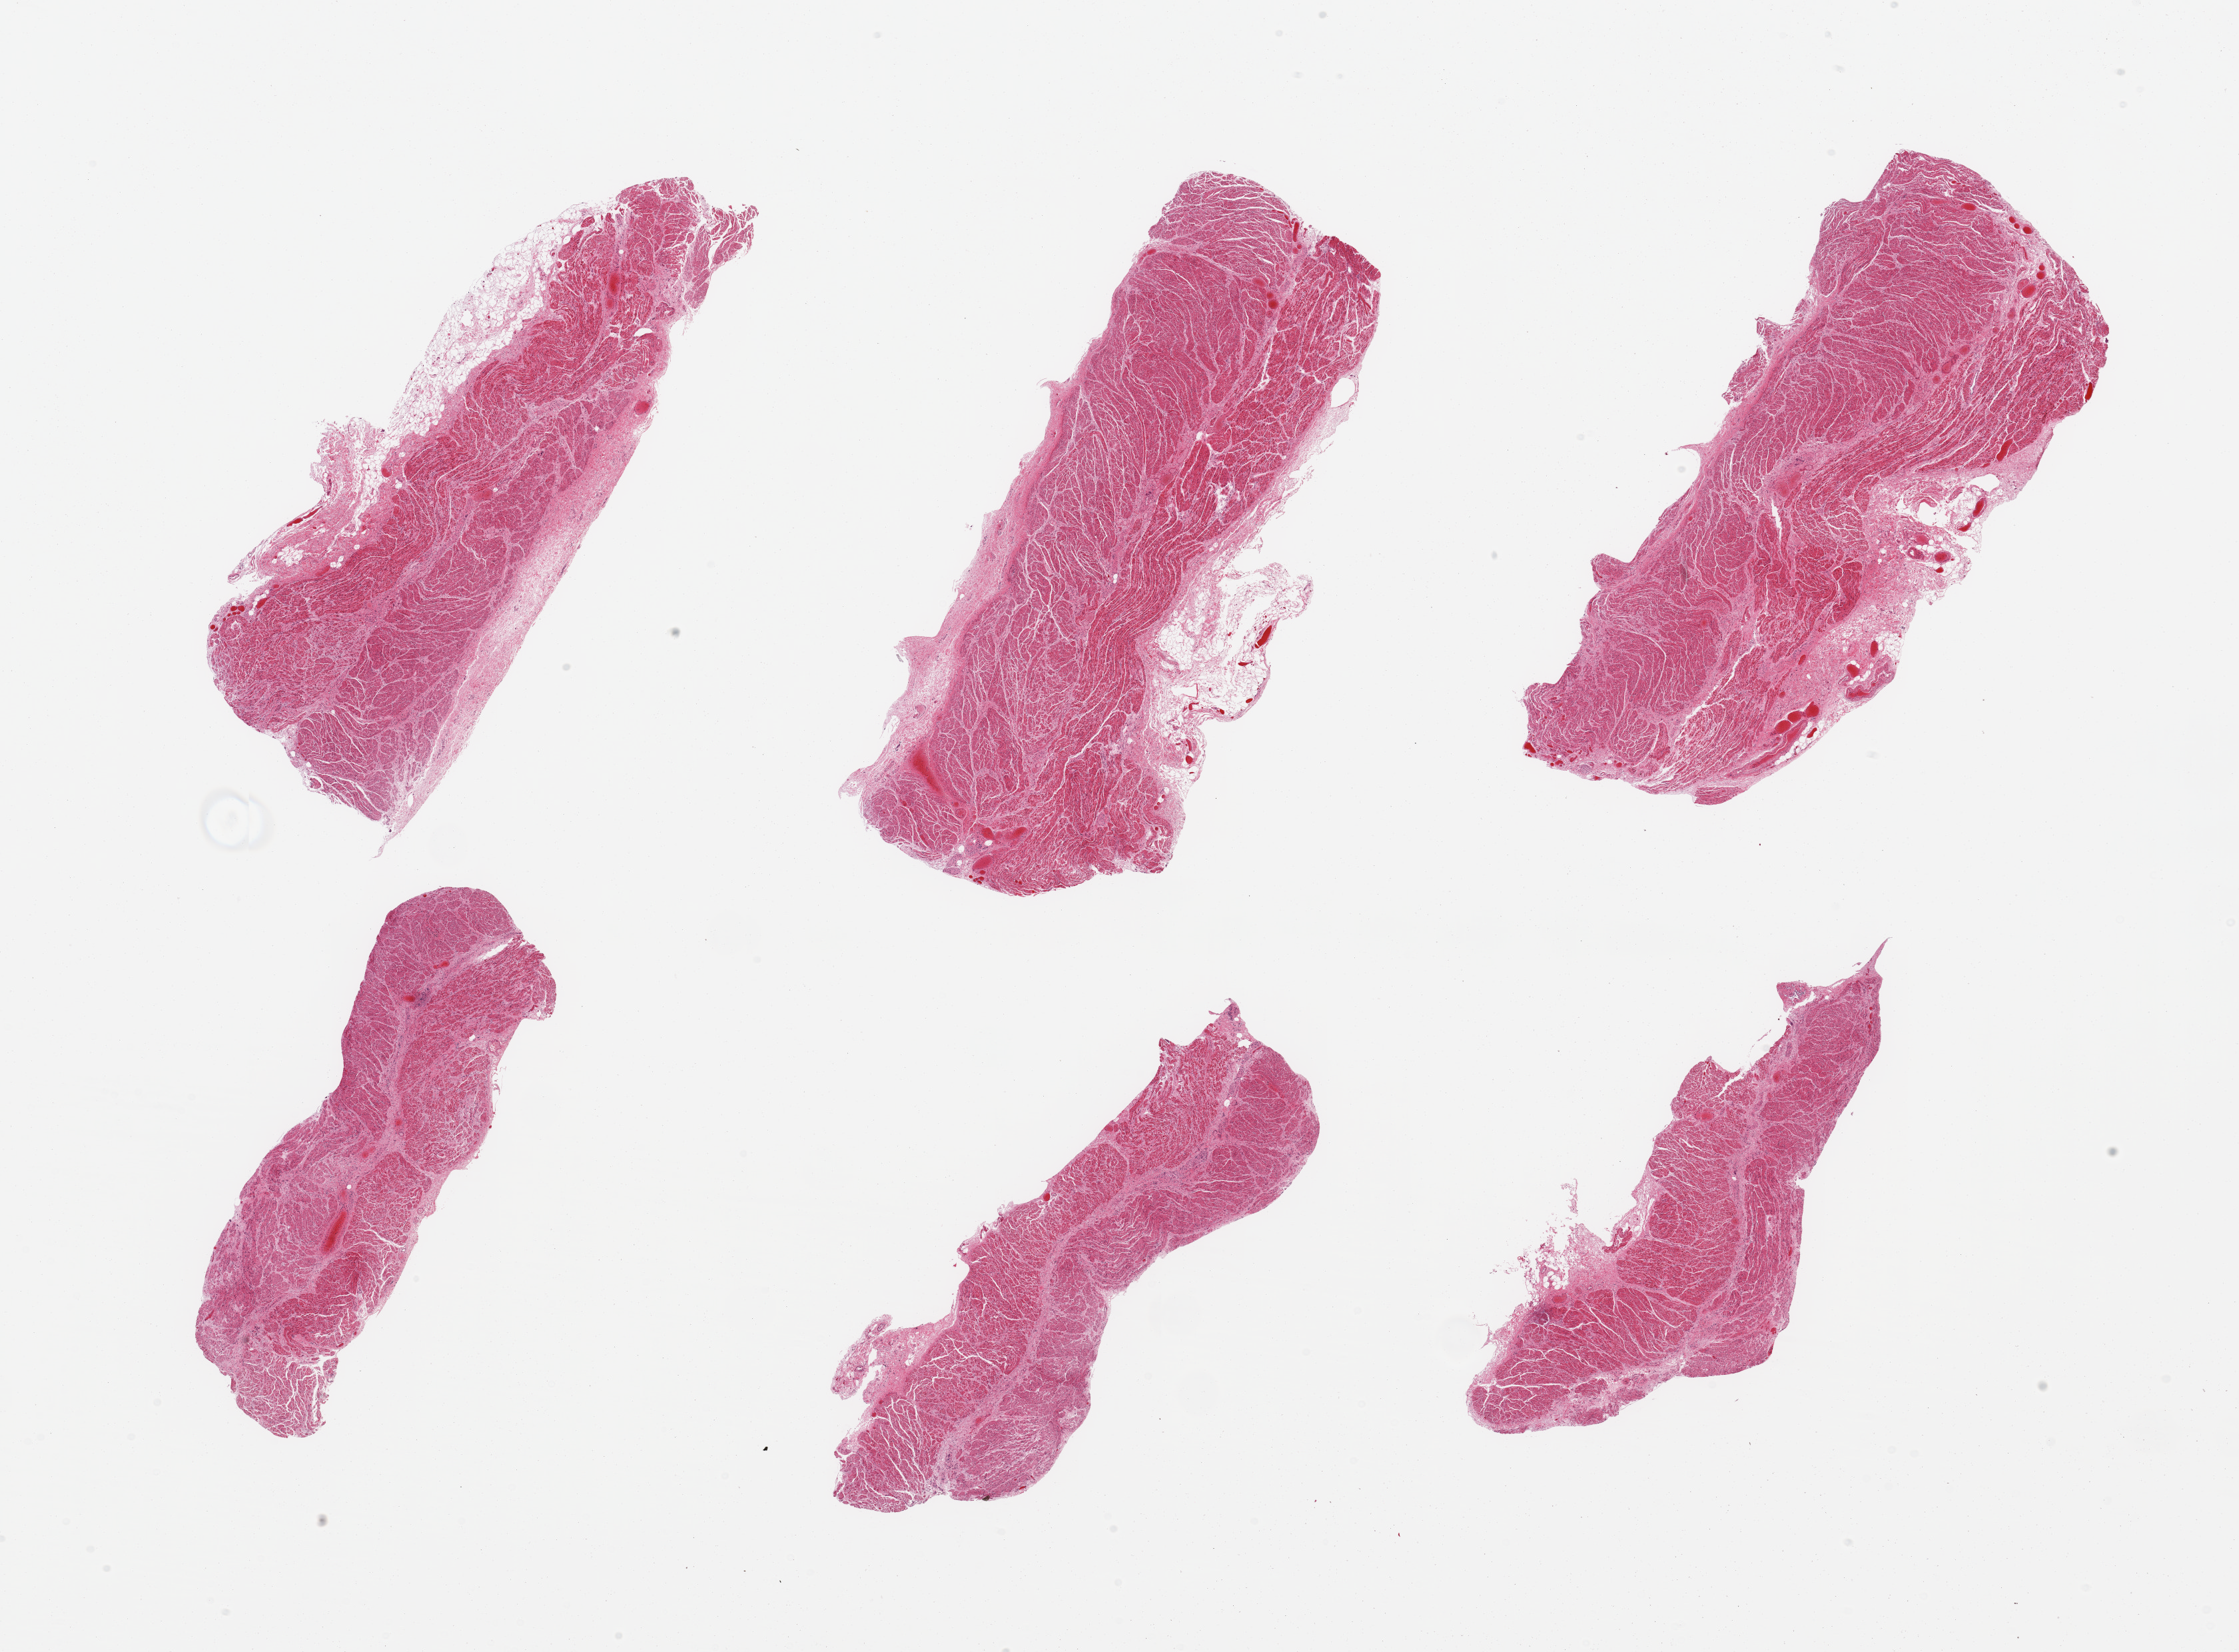
H&E whole-slide image, brightfield — a low-resolution overview of the entire scanned area, about 26.6 x 19.6 mm; PAXgene-fixed, paraffin-embedded tissue; target tissue: gastroesophageal junction; donor tissue sample. Female donor.
* pathologist's review note for this sample: 6 pieces, confirmed target muscularis; adherent serosa/fat up to ~0.6mm